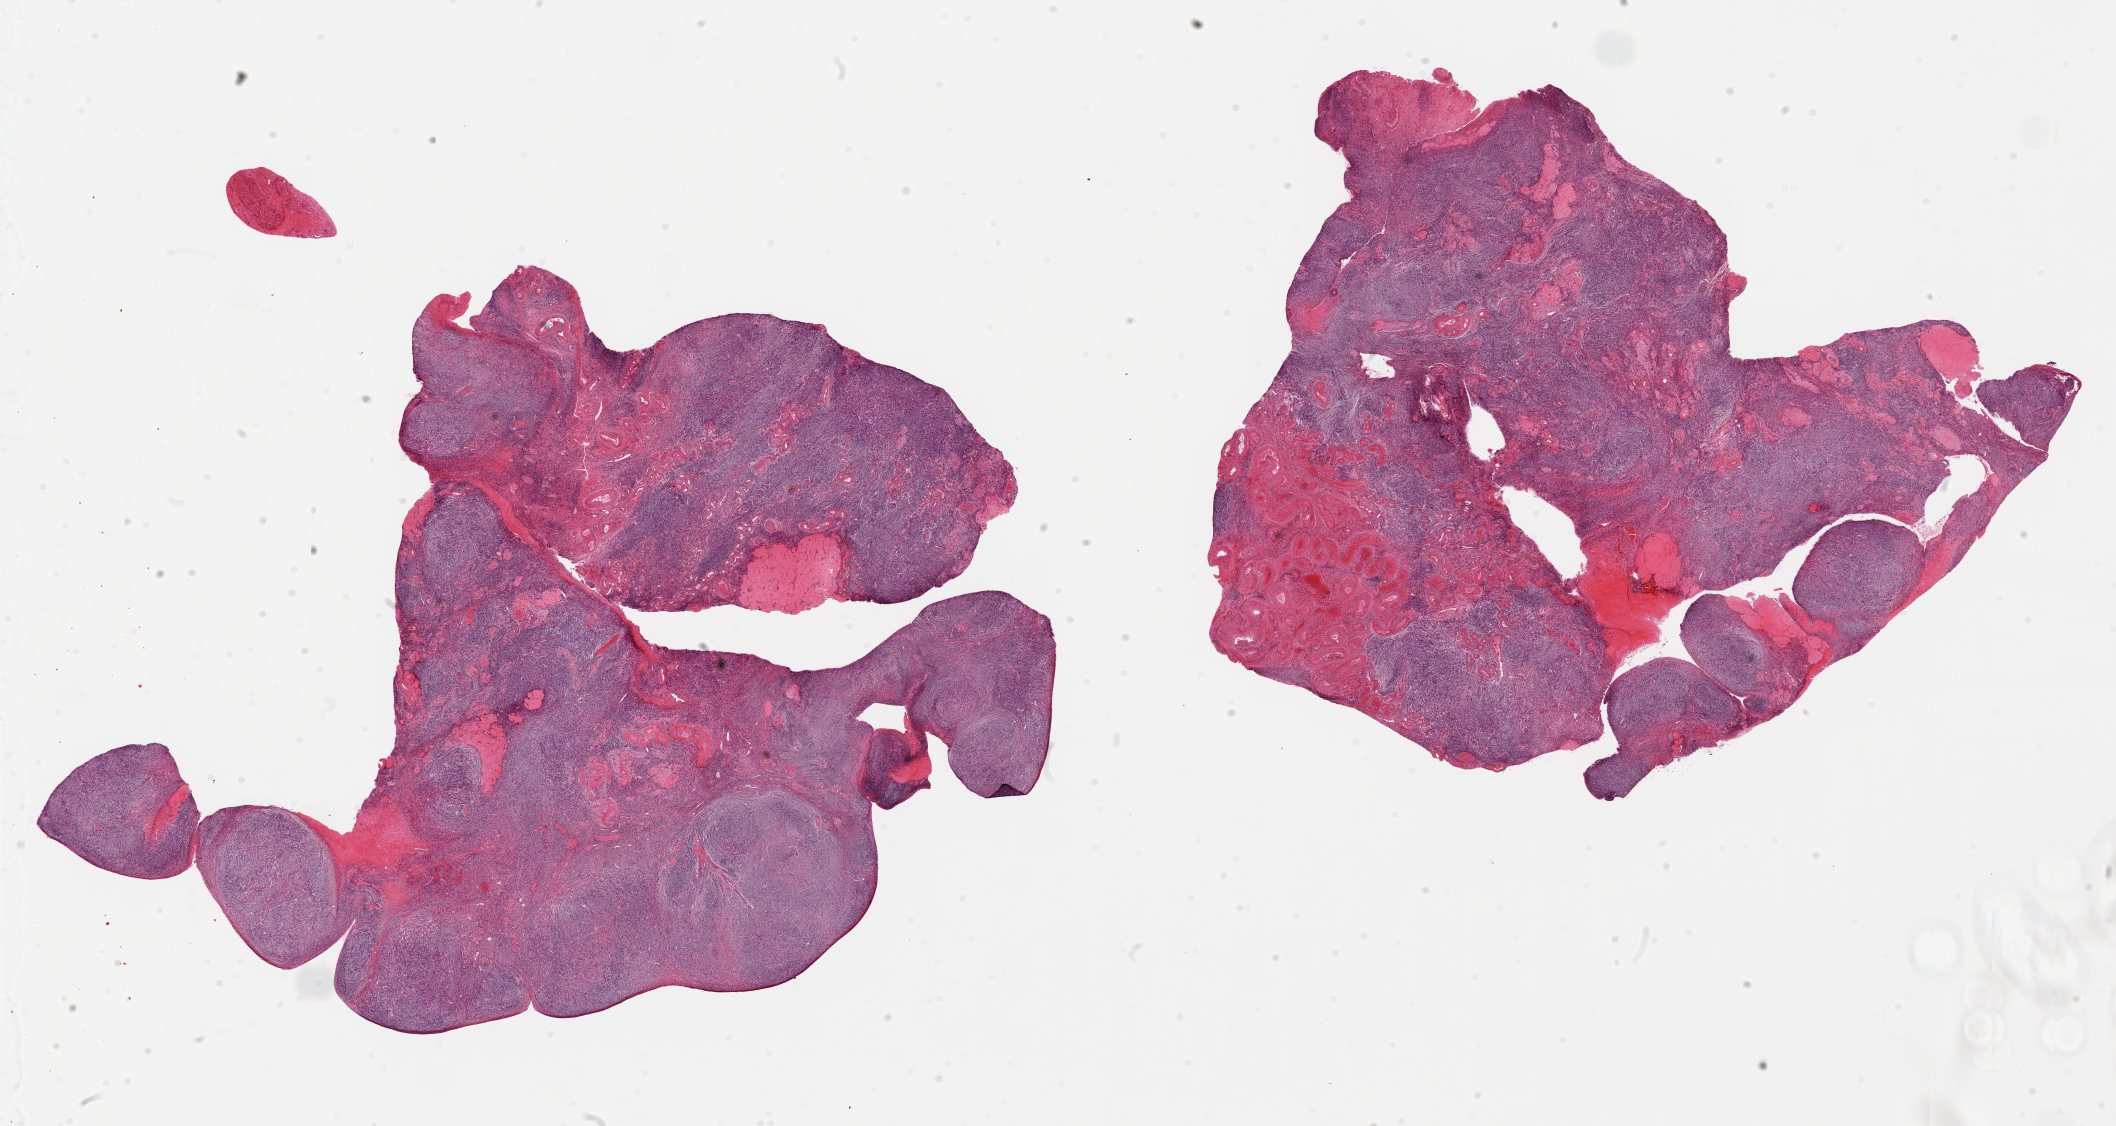
Hematoxylin and eosin (H&E) whole-slide image — low-resolution overview of the scanned area, about 33.5 x 17.8 mm, PAXgene-fixed paraffin-embedded (PFPE) section, sampled site (target tissue): ovary, tissue donor sample.
* review note (as recorded): 2 pieces; atrophic